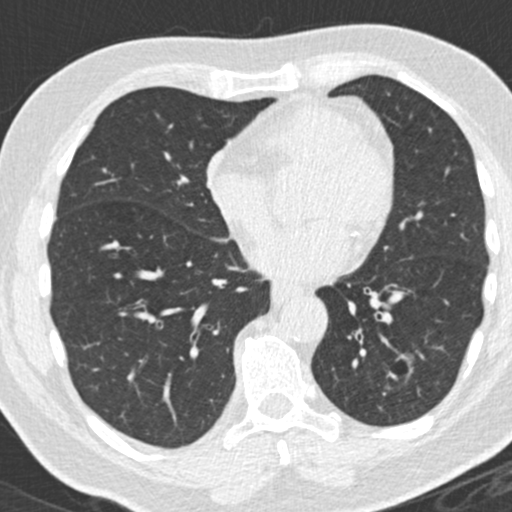
Axial slice from a low-dose chest CT screening exam, third annual screen, lung window (W 1500 / L -600 HU). Male, age 66 years at enrolment. Former smoker at enrolment.
Expert-annotated lung lesion, bounding box <355,343,427,429> (left, top, right, bottom; pixels). Reader record for this screening exam (exam-level; its link to the box is not recorded): non-calcified nodule or mass ≥4 mm, left lower lobe, 31 × 24 mm, spiculated (stellate) margins, pre-existing on the prior screen: yes; interval growth: yes. Participant outcome: lung cancer diagnosed 56 days after this screen — adenocarcinoma, NOS, left lower lobe, poorly differentiated (G3), stage IB (AJCC 6th edition), 38 mm at pathology.